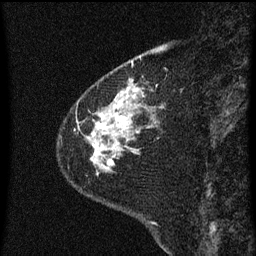
Breast MRI (dynamic contrast-enhanced), one sagittal slice; slice 14 of 60 in the series (ordered by position); dynamic contrast-enhanced series, image 2 of 3 at this slice position (ordered by acquisition); 1.5 T; TE 4.2 ms, TR 8 ms; 2 mm slice thickness; 256 × 256 image matrix. Patient: female, 60 years.
Outlined on this slice (semi-automatically segmented with operator editing):
- analysis volume of interest (the breast-tissue region the enhancement analysis was run in; not a lesion): bounding box [x1, y1, x2, y2] px = [77, 82, 156, 175]
- tumour enhancement mask (voxels above the 70 % enhancement threshold inside the analysis volume of interest): [94, 92, 136, 155]